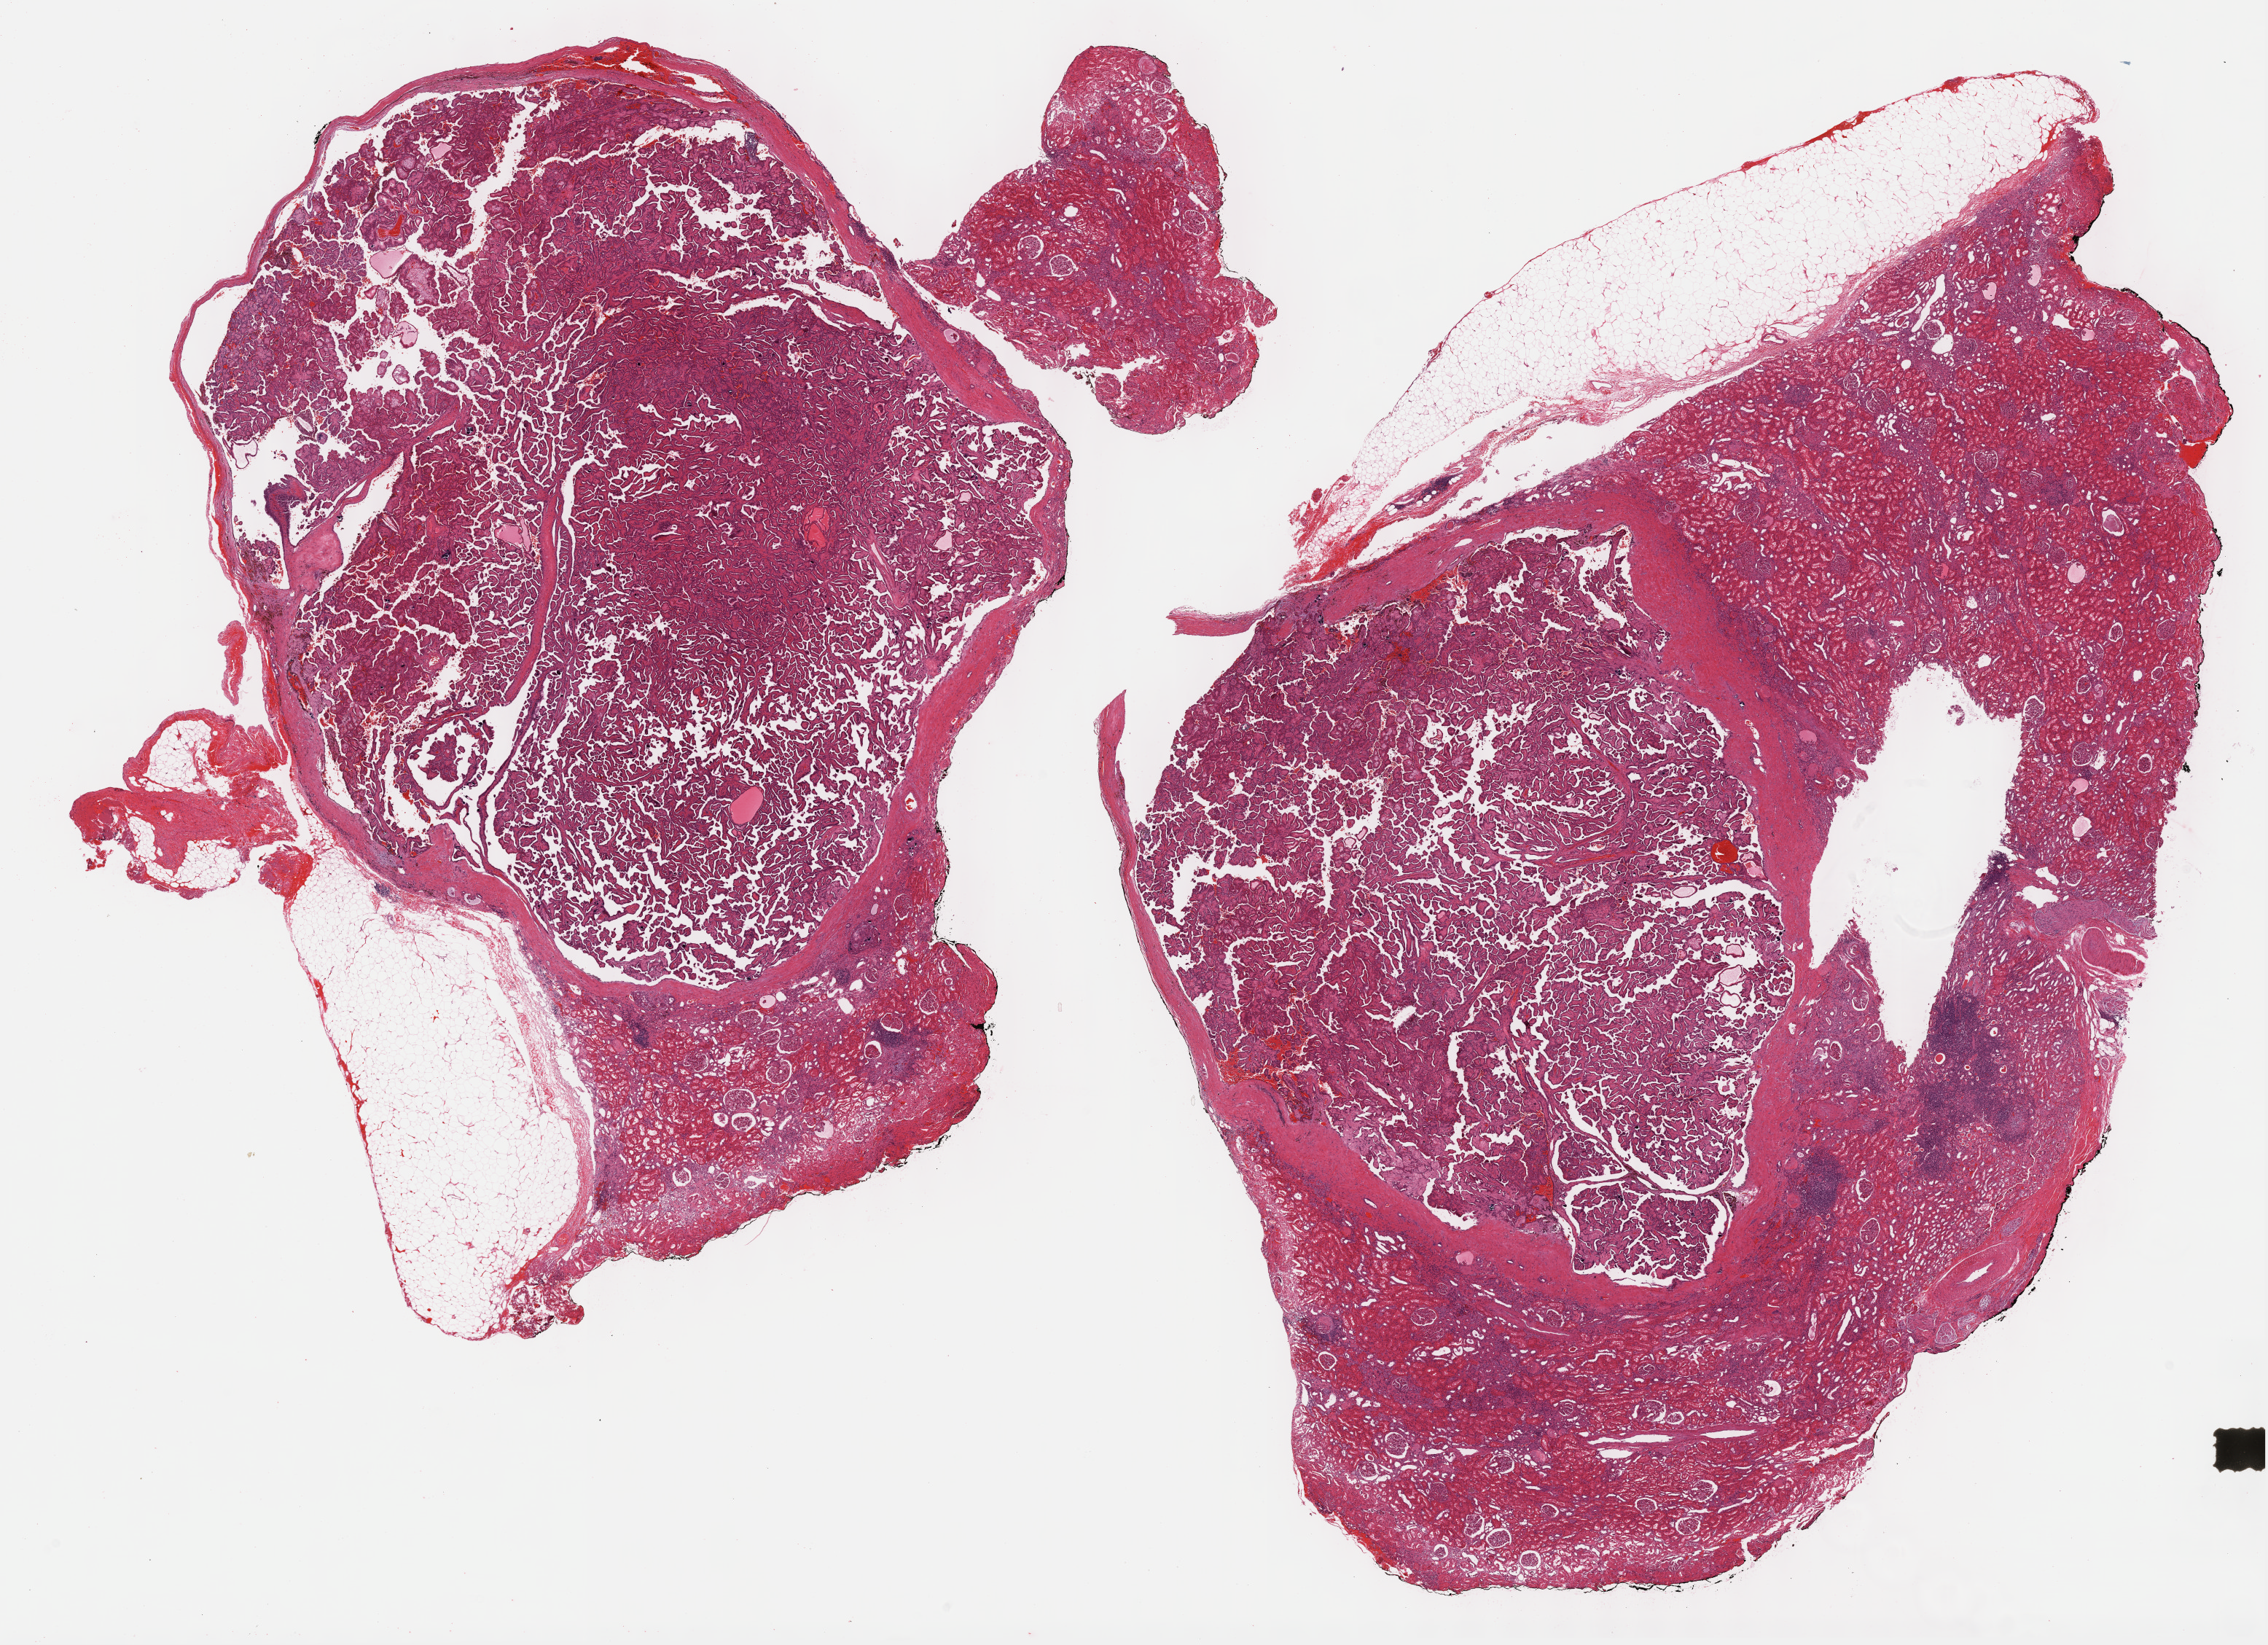
Whole-slide histology image, H&E, shown as a low-resolution overview of the whole scanned area (about 25.2 x 18.3 mm, from a 40x scan); formalin-fixed paraffin-embedded (FFPE) diagnostic section; primary tumour sample from the kidney. Patient: male, age at initial diagnosis 55 years.
Histologic diagnosis: Papillary adenocarcinoma, NOS. TNM: T1 N0 MX. AJCC pathologic stage: I (7th edition).